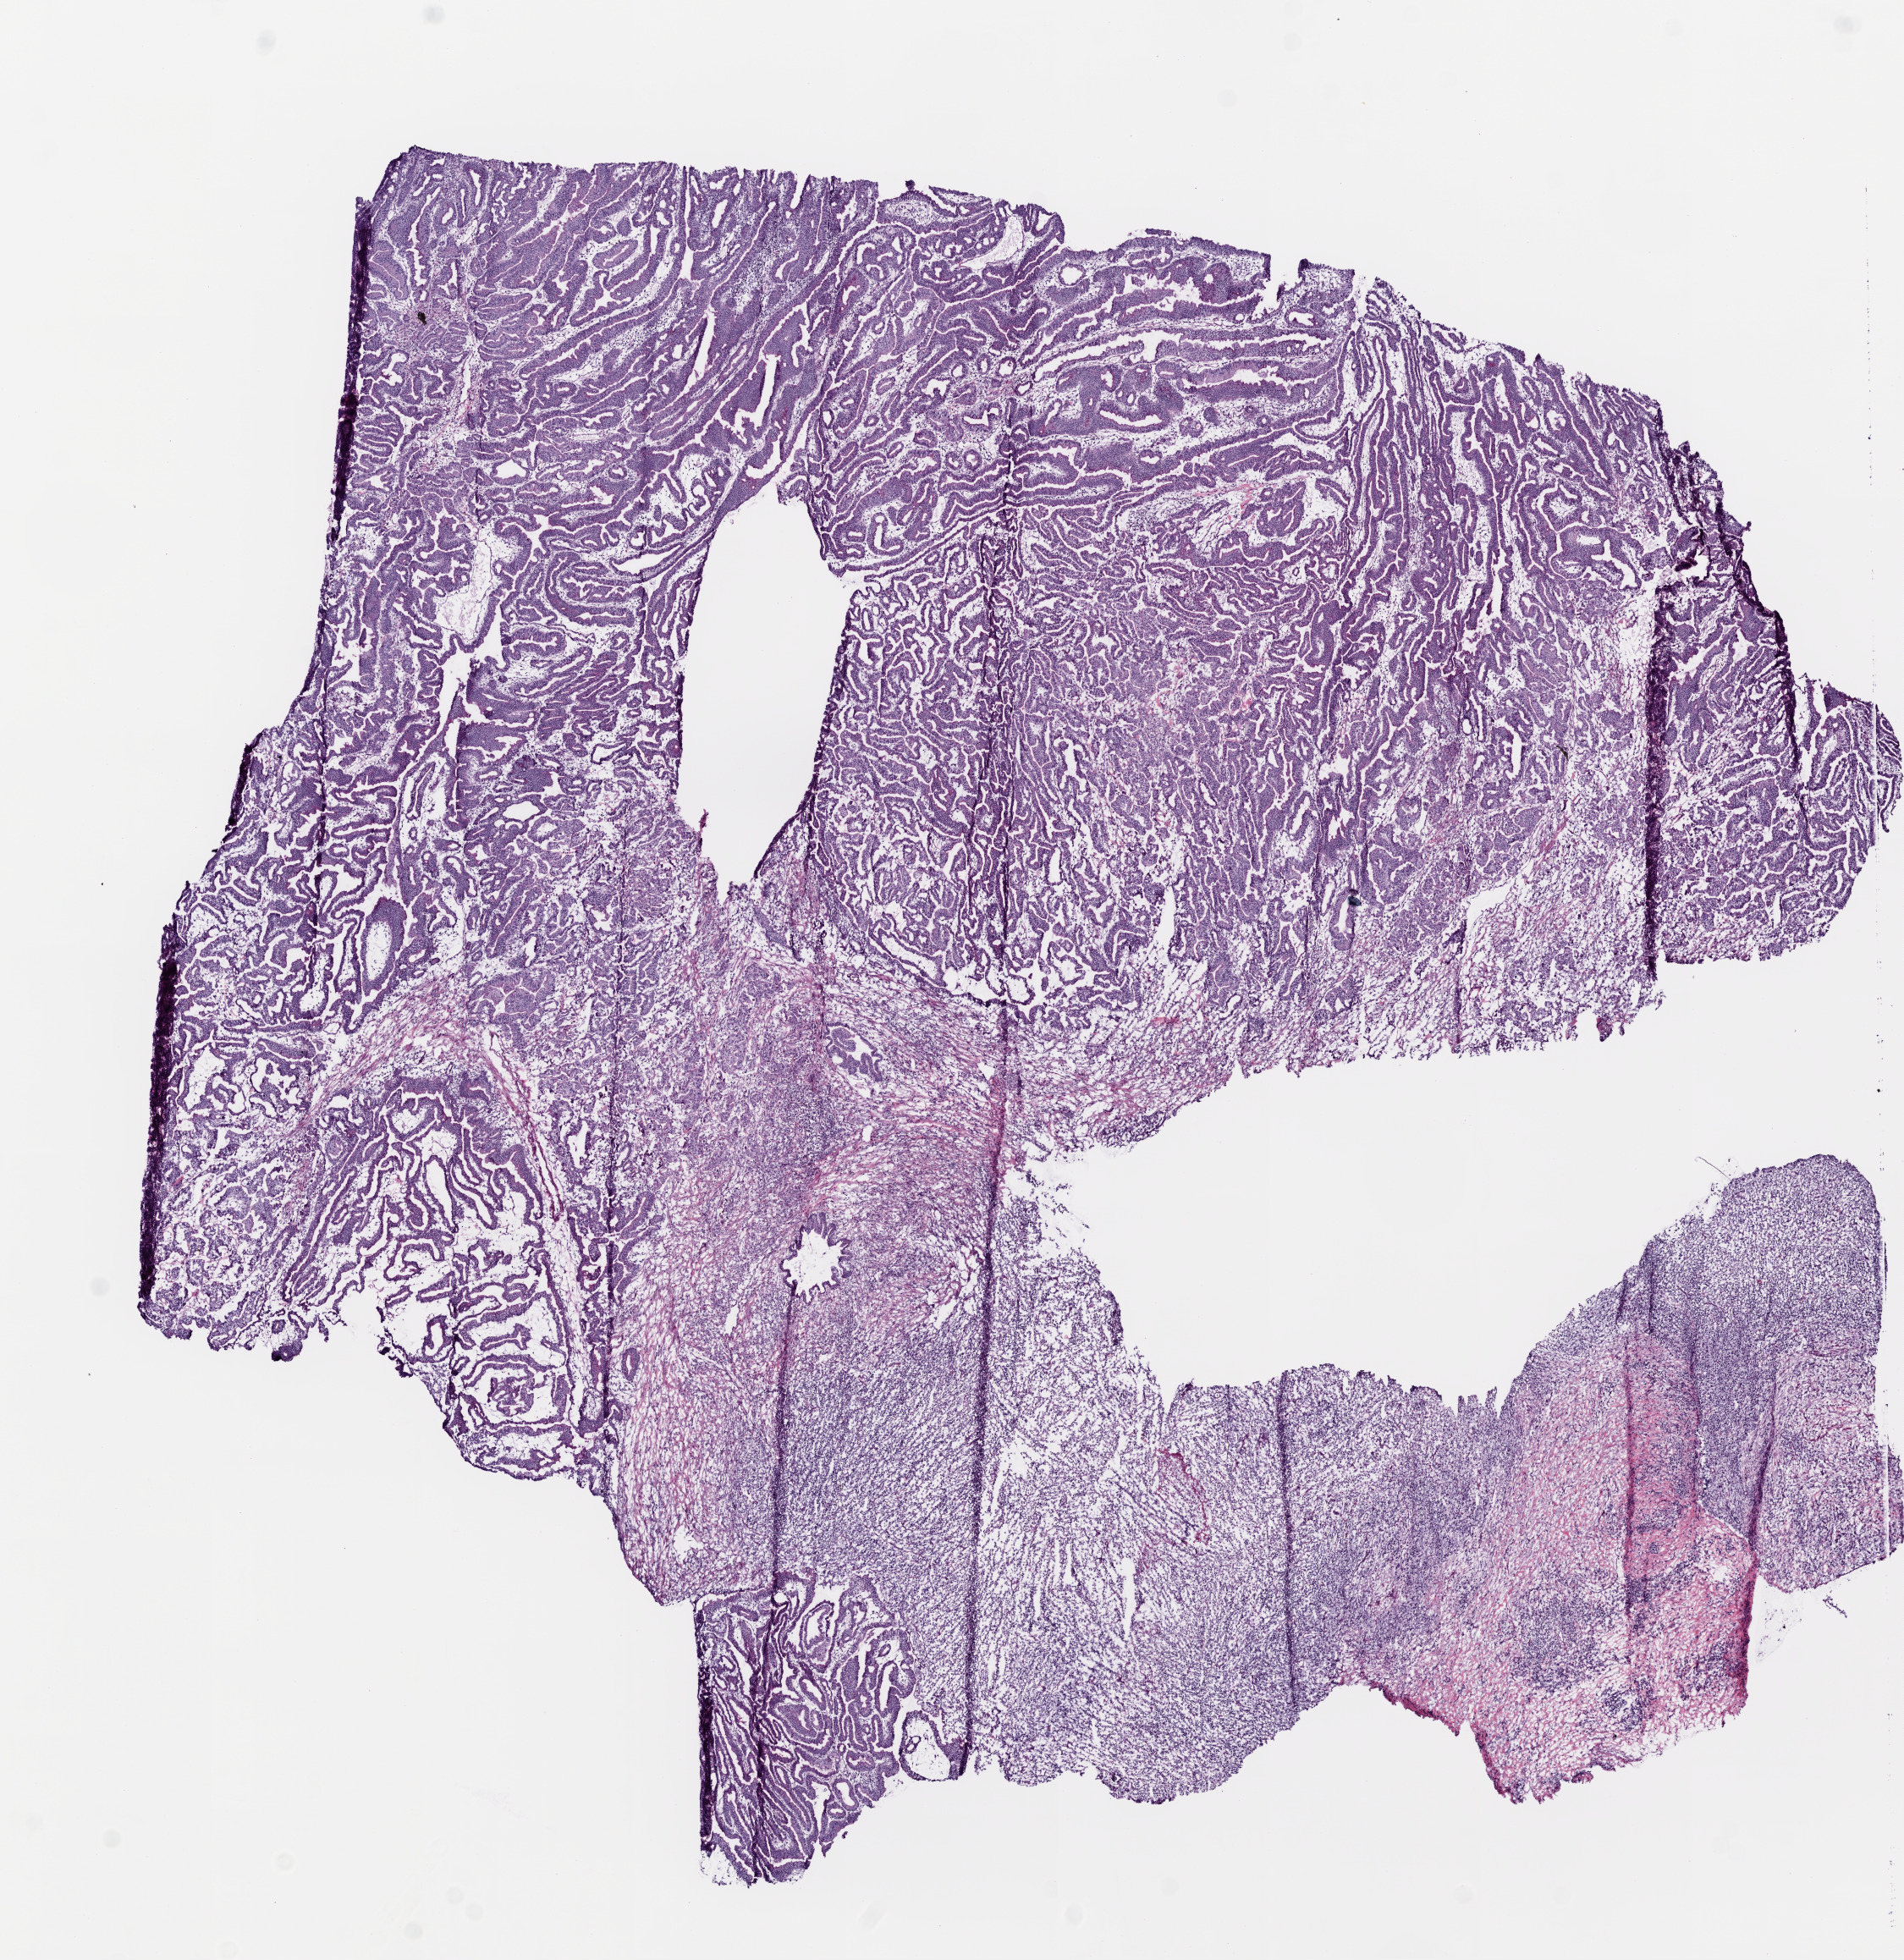
Whole-slide histology image, H&E, a low-resolution overview of the entire scanned area, about 9.0 x 9.3 mm; frozen section from the top of the tissue portion; primary tumour sample from the stomach. Male patient; age at initial diagnosis 84 years. Histologic grade: G2 (moderately differentiated). Slide review estimates, as recorded: tumour cells 85%, tumour nuclei 75%, normal cells 0%, stromal cells 15%, necrosis 0%. Infiltration values recorded for this section: lymphocyte infiltration 10%, monocyte infiltration 0%, neutrophil infiltration 0%.
AJCC pathologic stage: IB. Diagnosis: Adenocarcinoma, NOS (cardia, NOS).